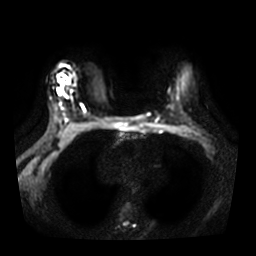
Breast MRI, one axial slice; position 21 of 31 along the scan axis; diffusion-weighted series; image 2 of 4 stored at this slice position (different b-values; order by instance number); 3 T; 5 mm slice thickness; 256 × 256 image matrix, field of view 350 × 350 mm. Female patient.
Structures marked on this image (expert manual segmentation):
- tumour on diffusion-weighted imaging: bounding box (x1, y1, x2, y2) in pixels: (58, 79, 63, 93)